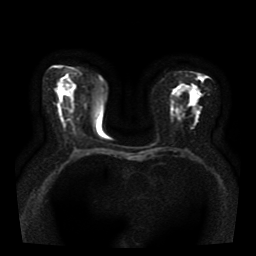
Breast MRI, one axial slice. Slice 20 of 41 in the series (ordered by position). Diffusion-weighted series; image 2 of 4 stored at this slice position (different b-values; order by instance number). 1.5 T. 256 × 256 image matrix, field of view 330 × 330 mm. Female patient.
Annotated regions visible in this slice (manually delineated by an expert):
- tumour on diffusion-weighted imaging: bounding box (x1, y1, x2, y2) in pixels: (195, 92, 200, 98)